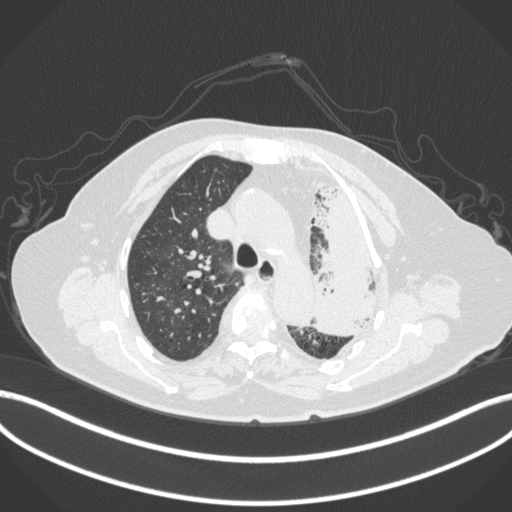
Chest CT, one axial slice; slice 288 of 399 in the series (ordered by position); reconstruction kernel B31f; lung window (W 1500 / L -600 HU); 512 × 512 image matrix, field of view 400 × 400 mm. Female patient, age 75 years. From the clinical record (not read from this slice): clinical TNM (as recorded): T3 N3 M1.
Outlined on this slice (bounding box drawn by a radiologist):
- lung tumour (recorded histology: adenocarcinoma): bounding box (x1, y1, x2, y2) in pixels: (312, 178, 391, 345)